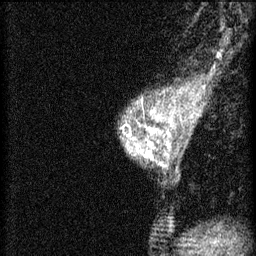
Breast MRI (dynamic contrast-enhanced), one sagittal slice. Position 38 of 46 along the scan axis. 3 images stored at this slice position (order not interpretable as contrast timing). 1.5 T. TE 4.2 ms, TR 8.2 ms. 256 × 256 image matrix, field of view 180 × 180 mm. Female patient, age 44 years.
Annotated regions visible in this slice (semi-automatic segmentation, software-assisted and operator-edited):
- analysis volume of interest (the breast-tissue region the enhancement analysis was run in; not a lesion): bounding box <119,128,156,165> (left, top, right, bottom; pixels)
- tumour enhancement mask (voxels above the 70 % enhancement threshold inside the analysis volume of interest): <127,130,156,161>